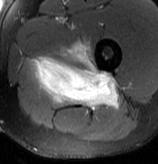
MRI of an extremity soft-tissue mass, one axial slice; slice 53 of 70 in the series (ordered by position); T2-weighted fat-saturated; MR volume resampled by the dataset authors to the PET/CT grid (not the native acquisition matrix); 3.27 mm slice thickness; 158 × 164 image matrix, field of view 154 × 160 mm. Male patient. From the clinical record (not read from this slice): histological type: extraskeletal osteosarcoma; grade: high; site of the primary tumour: left adductur.
Outlined on this slice (expert contour drawn on MRI and transferred to this co-registered scan by the dataset authors):
- gross tumour volume (mass): box from (x=29, y=41) to (x=119, y=109) px